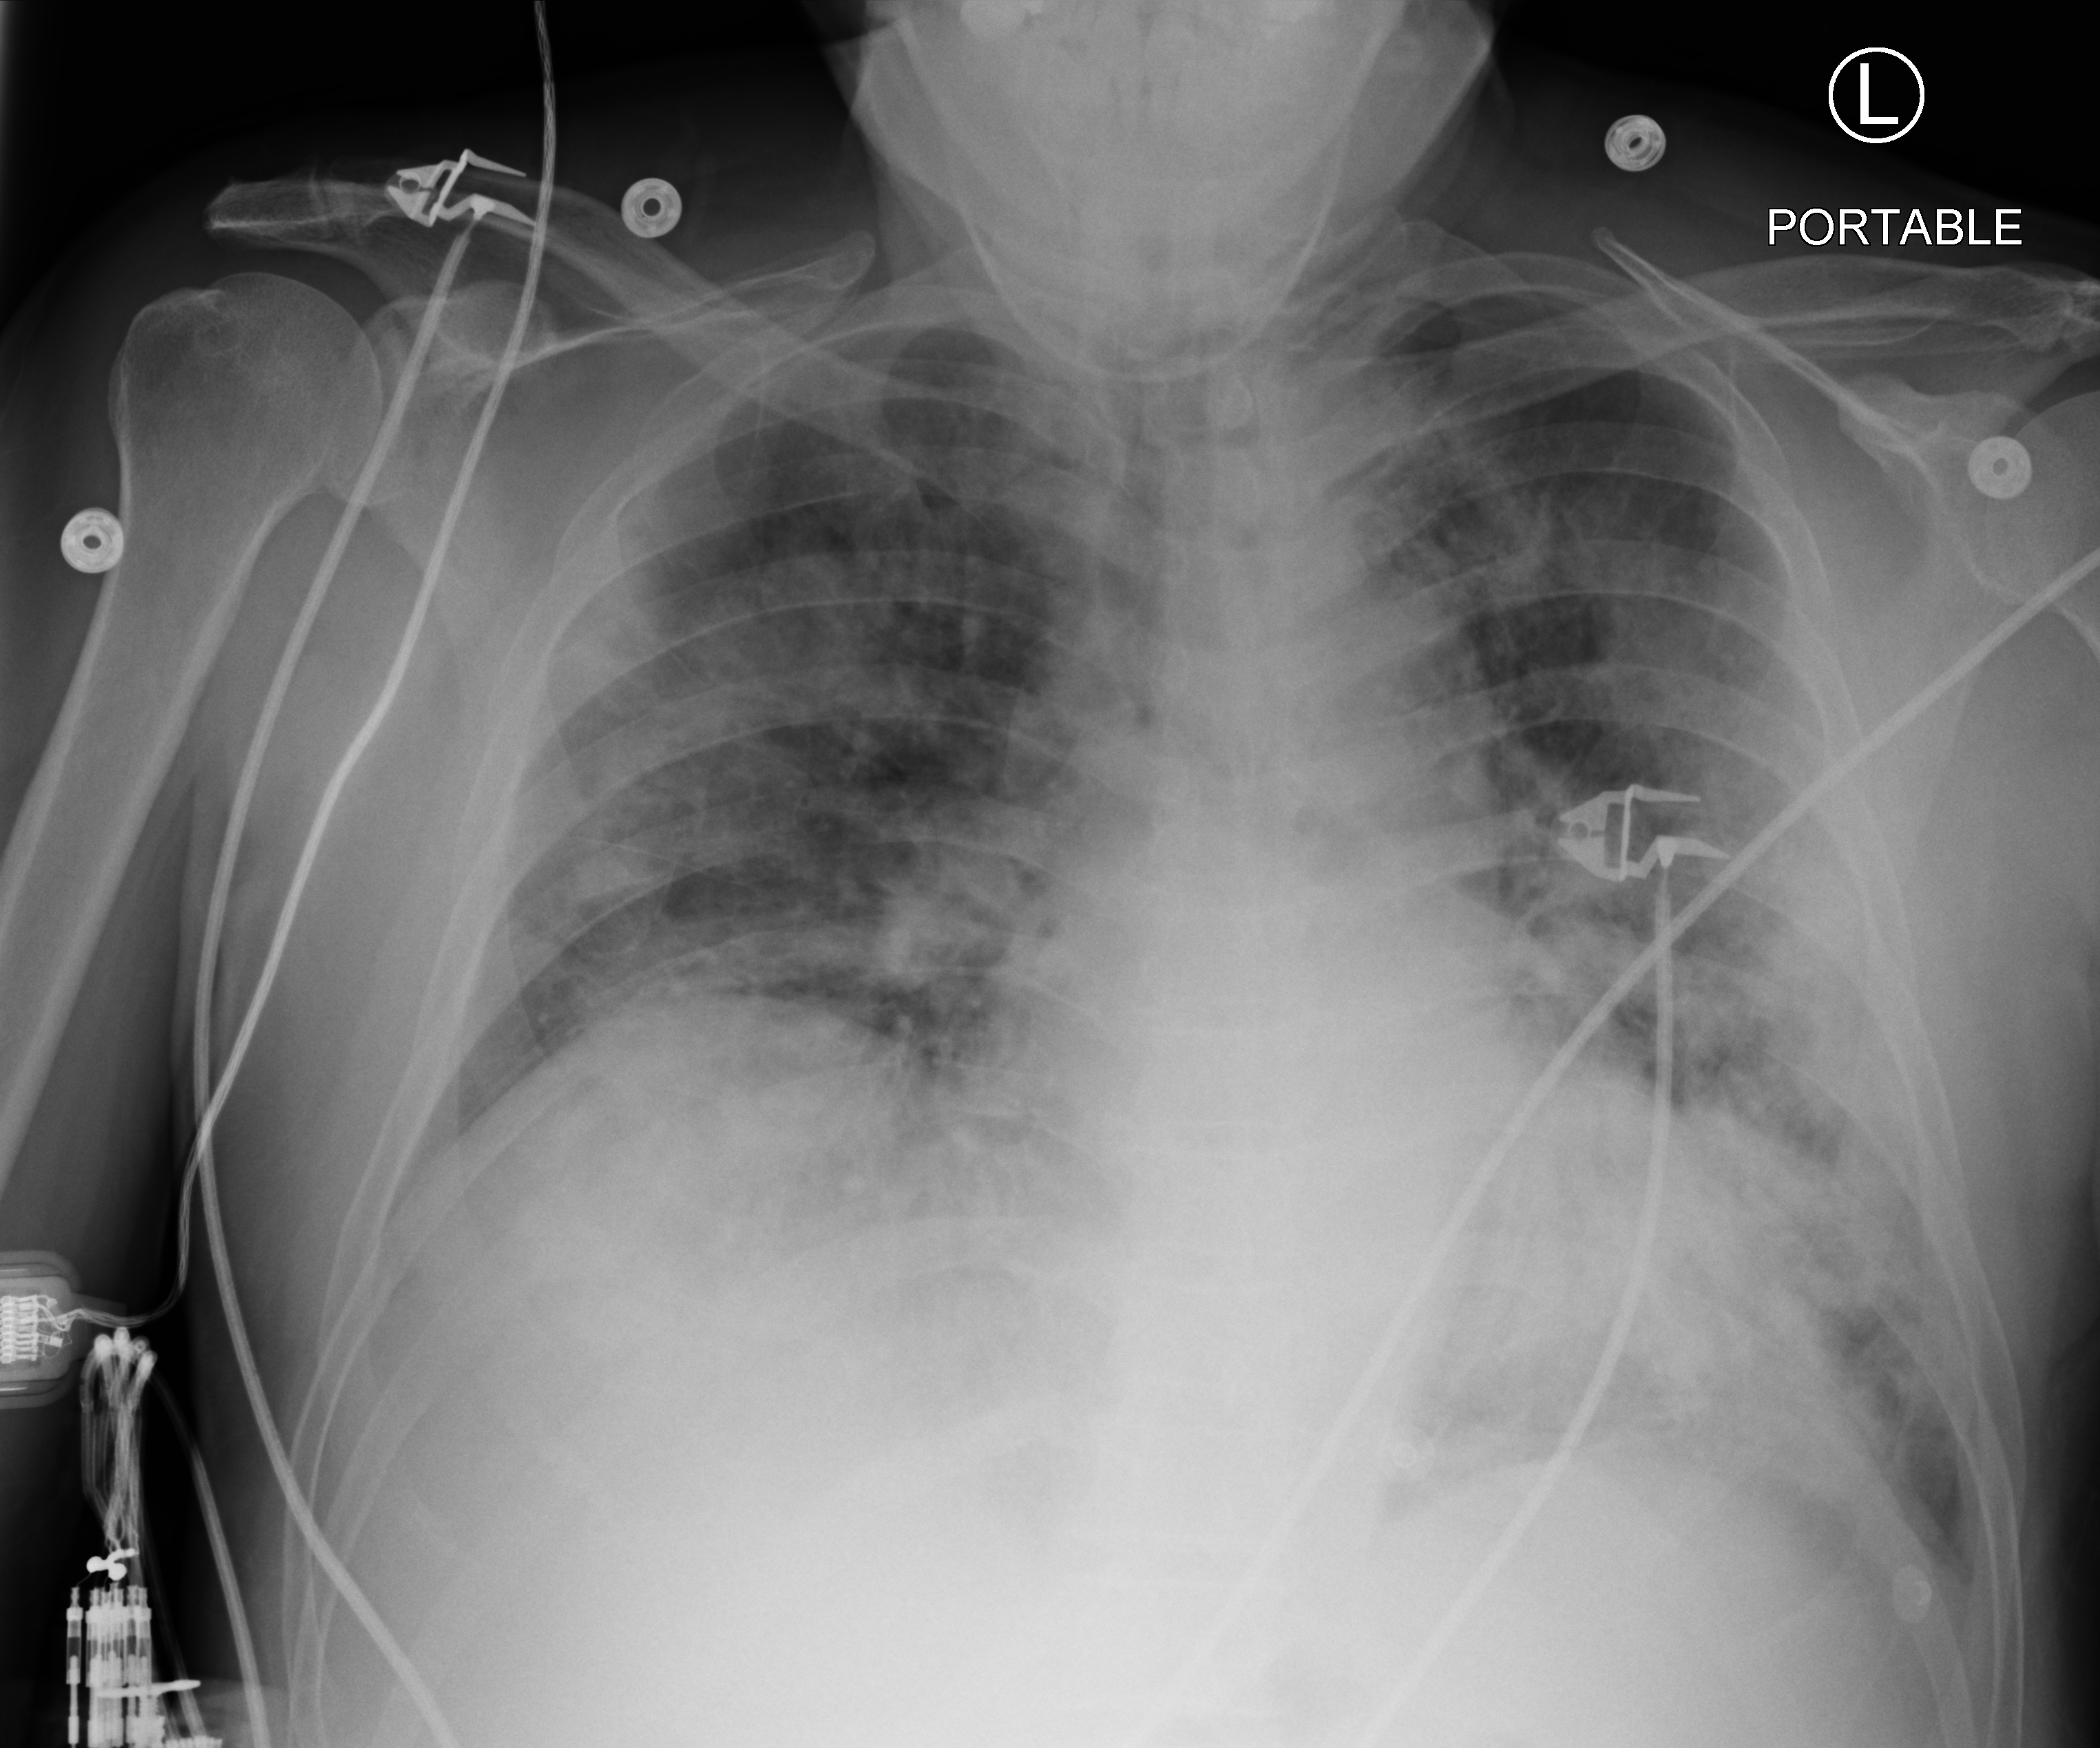
Portable chest radiograph, anteroposterior (AP) projection. Male patient hospitalised with COVID-19, age 60–74 years.
Admission-level facts for this patient (not findings on this image; timing relative to this image not recorded): COPD (admission record): no; mechanically ventilated during this hospital stay: no; other chronic lung disease (admission record): no.